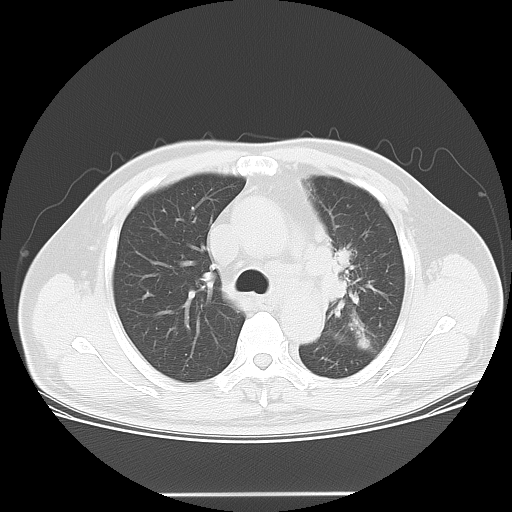
Chest CT, one axial slice; slice 39 of 55 in the series (ordered by position); reconstruction kernel LUNG; lung window (W 1500 / L -600 HU); 5 mm slice thickness; 512 × 512 image matrix. Patient: male, 61 years. Case-level facts recorded for this patient, not image findings: clinical TNM (as recorded): T3 N1 M1; histopathological grade: G3.
Structures marked on this image (rectangle marked by the reading radiologist):
- lung tumour (recorded histology: small cell carcinoma): box from (x=319, y=238) to (x=366, y=315) px